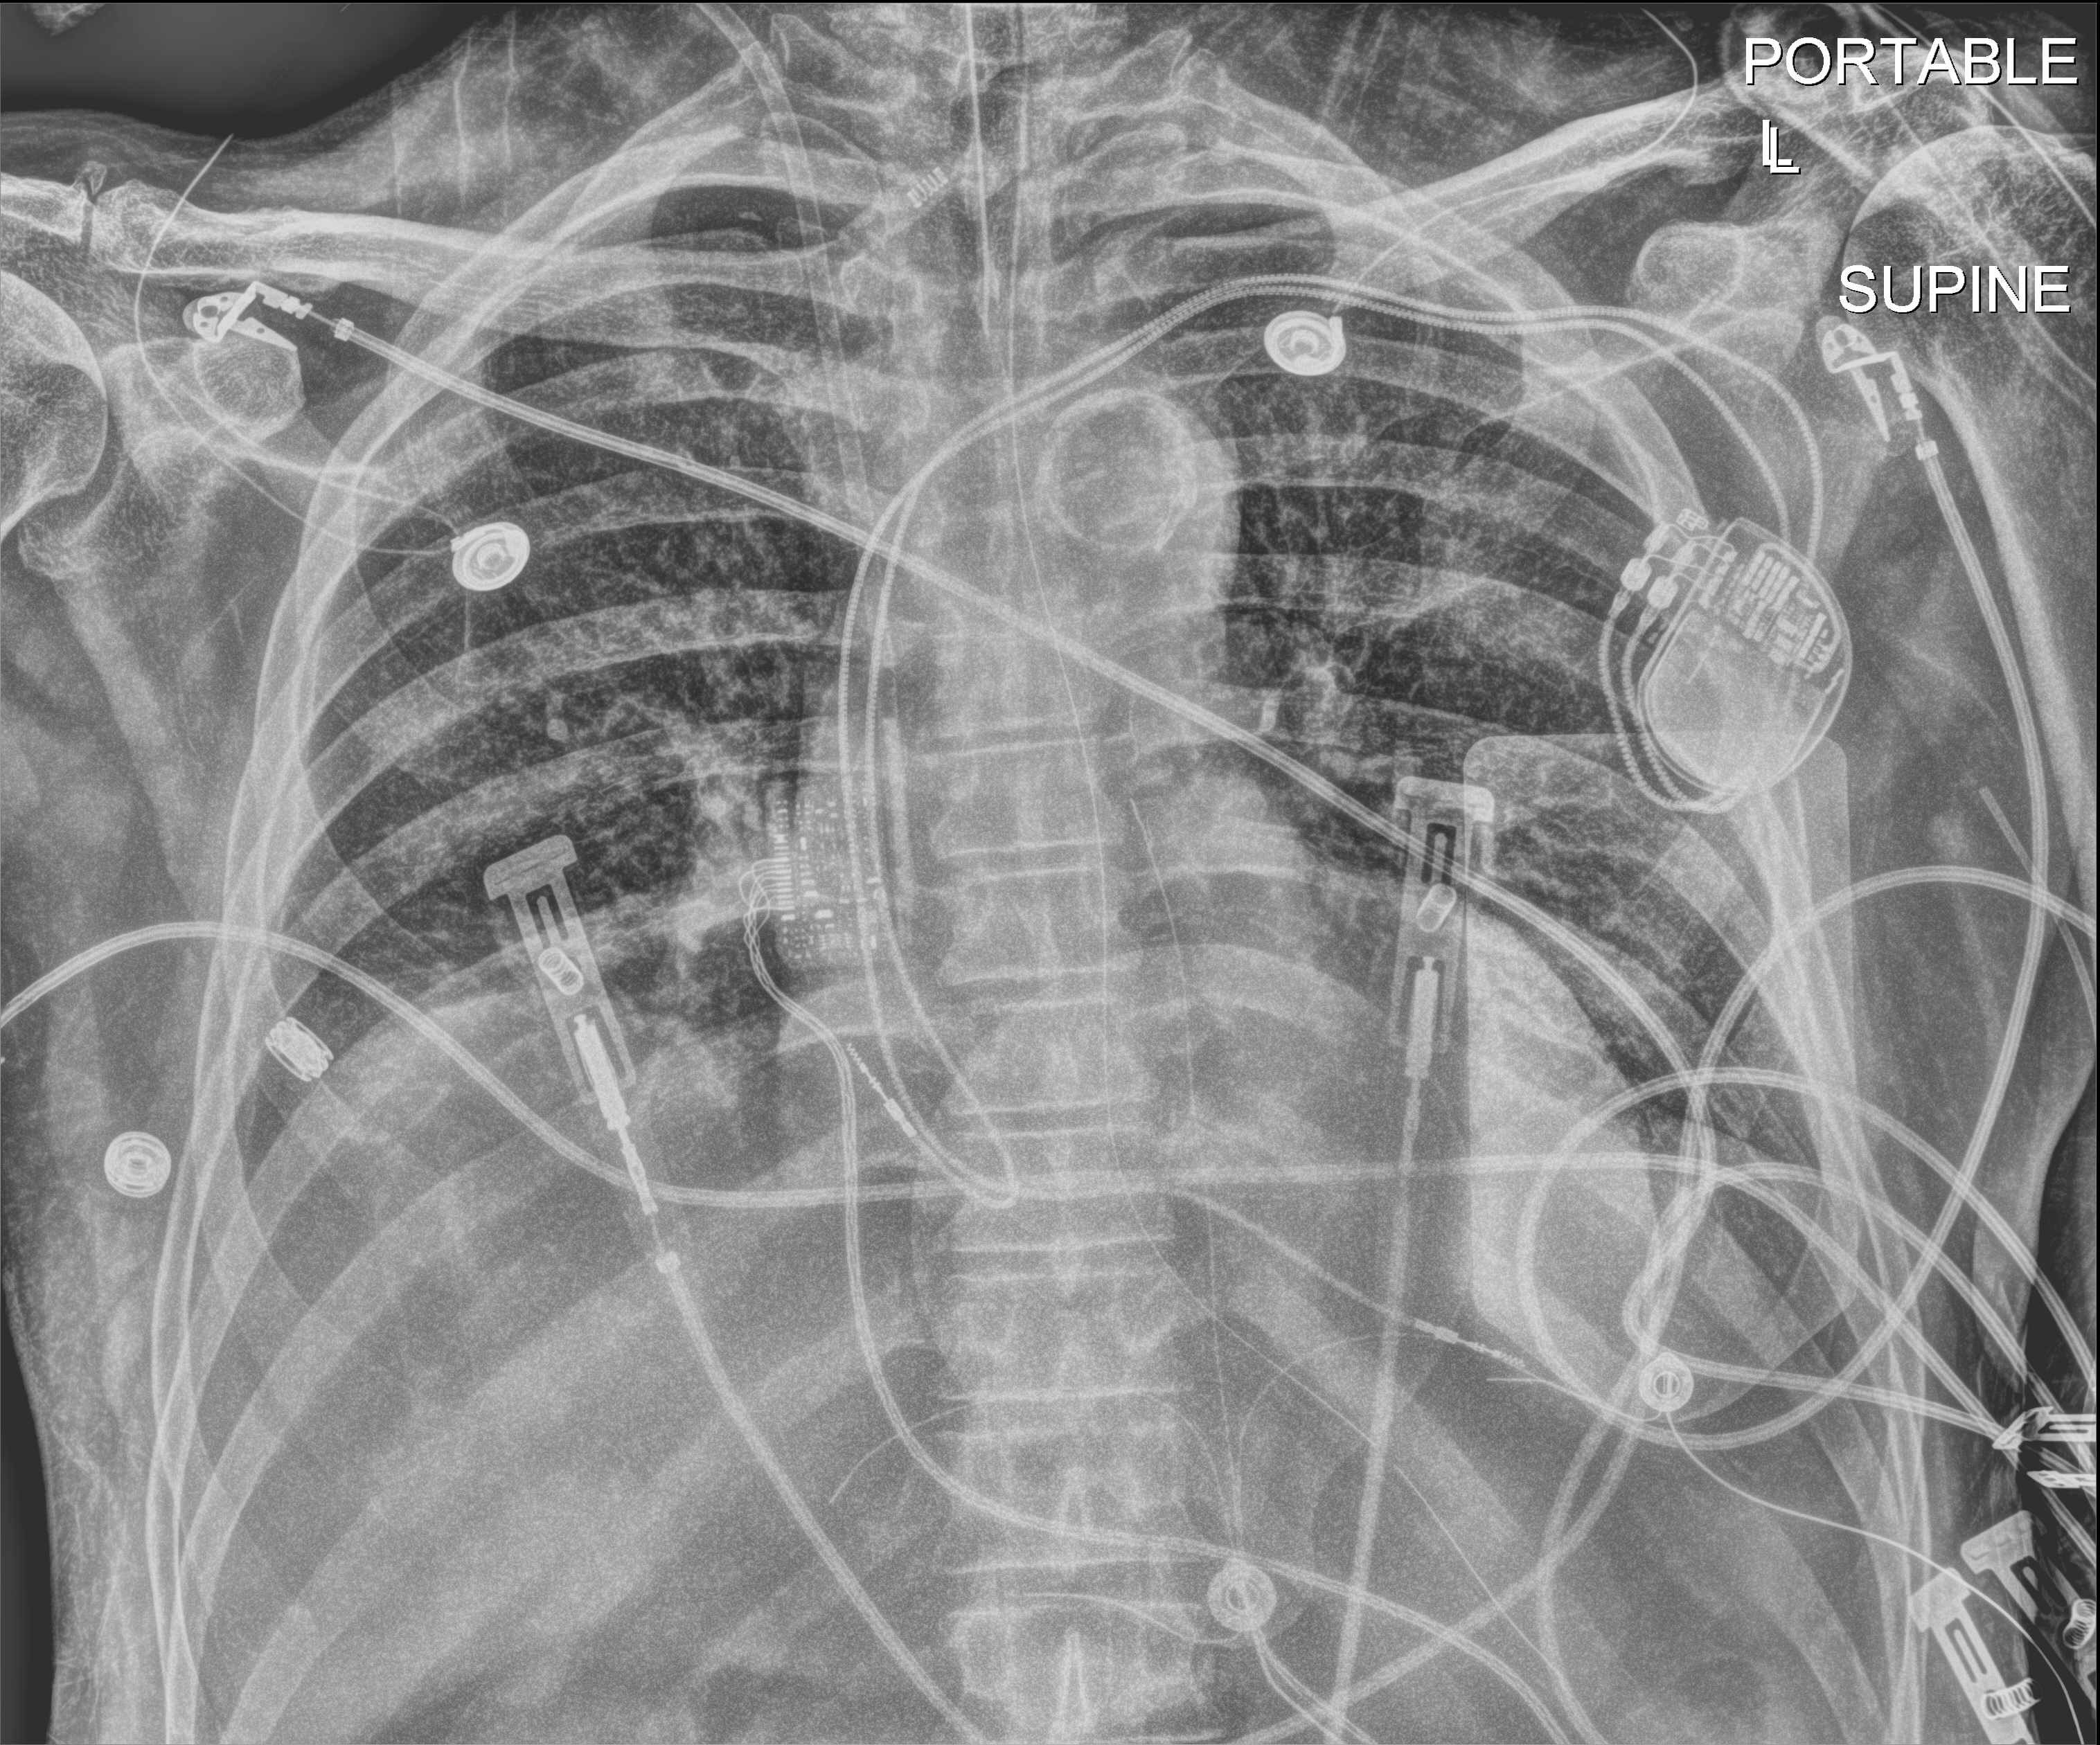
Portable chest radiograph, anteroposterior (AP) projection. Male patient hospitalised with COVID-19, age 60–74 years.
Hospital-stay facts (about this admission, not read from this image; timing relative to this image not recorded):
- mechanically ventilated during this hospital stay: yes